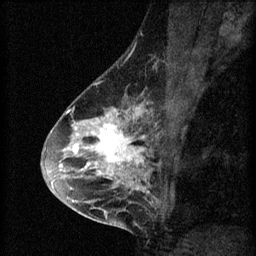
Breast MRI (dynamic contrast-enhanced), one sagittal slice; position 36 of 60 along the scan axis; 3 images stored at this slice position (order not interpretable as contrast timing); 1.5 T; TE 4.2 ms, TR 8.2 ms; 256 × 256 image matrix, field of view 180 × 180 mm. Patient: female, 45 years.
Structures marked on this image (semi-automatically segmented with operator editing):
- analysis volume of interest (the breast-tissue region the enhancement analysis was run in; not a lesion): box from (x=54, y=104) to (x=155, y=217) px
- tumour enhancement mask (voxels above the 70 % enhancement threshold inside the analysis volume of interest): (x=54, y=106)–(x=149, y=211)